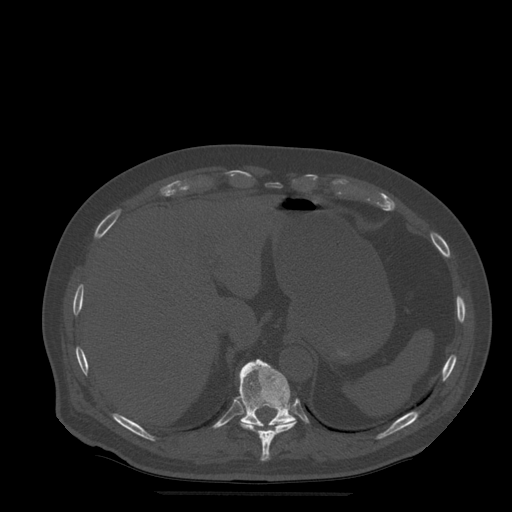
CT including the spine, one axial slice; position 256 of 522 along the scan axis; bone window (W 1800 / L 400 HU); 512 × 512 image matrix. Patient age 72 years. From the clinical record (not read from this slice): primary cancer: prostate.
Annotated regions visible in this slice (semi-automatically segmented with operator editing):
- T10 vertebra: box from (x=241, y=421) to (x=297, y=461) px
- T11 vertebra: (x=239, y=359)–(x=296, y=427)